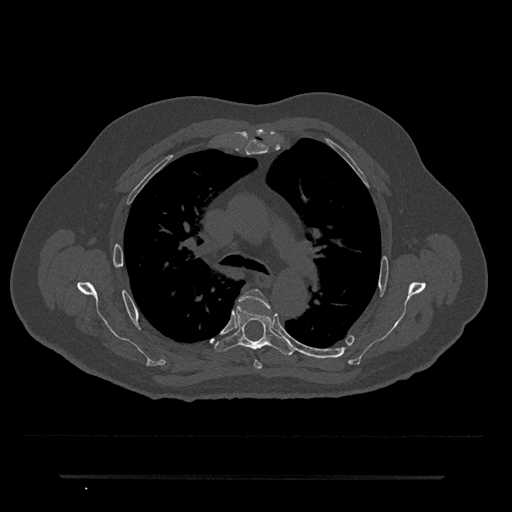
CT including the spine, one axial slice; reconstruction kernel Br40s/3; 120 kVp; bone window (W 1800 / L 400 HU); 512 × 512 image matrix, field of view 437 × 437 mm. Patient: male, 69 years. From the clinical record (not read from this slice): primary cancer: prostate.
Annotated regions visible in this slice (semi-automatically segmented with operator editing):
- T4 vertebra: bounding box [x1, y1, x2, y2] px = [240, 289, 270, 370]
- T5 vertebra: [214, 303, 295, 355]